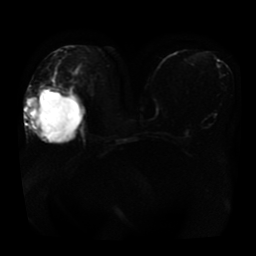
Breast MRI, one axial slice. Slice 23 of 41 in the series (ordered by position). Diffusion-weighted series; image 2 of 4 stored at this slice position (different b-values; order by instance number). 1.5 T. 5 mm slice thickness. 256 × 256 image matrix, field of view 360 × 360 mm. Female patient.
Annotated regions visible in this slice (manually delineated by an expert):
- tumour on diffusion-weighted imaging: bounding box [x1, y1, x2, y2] px = [27, 97, 40, 121]